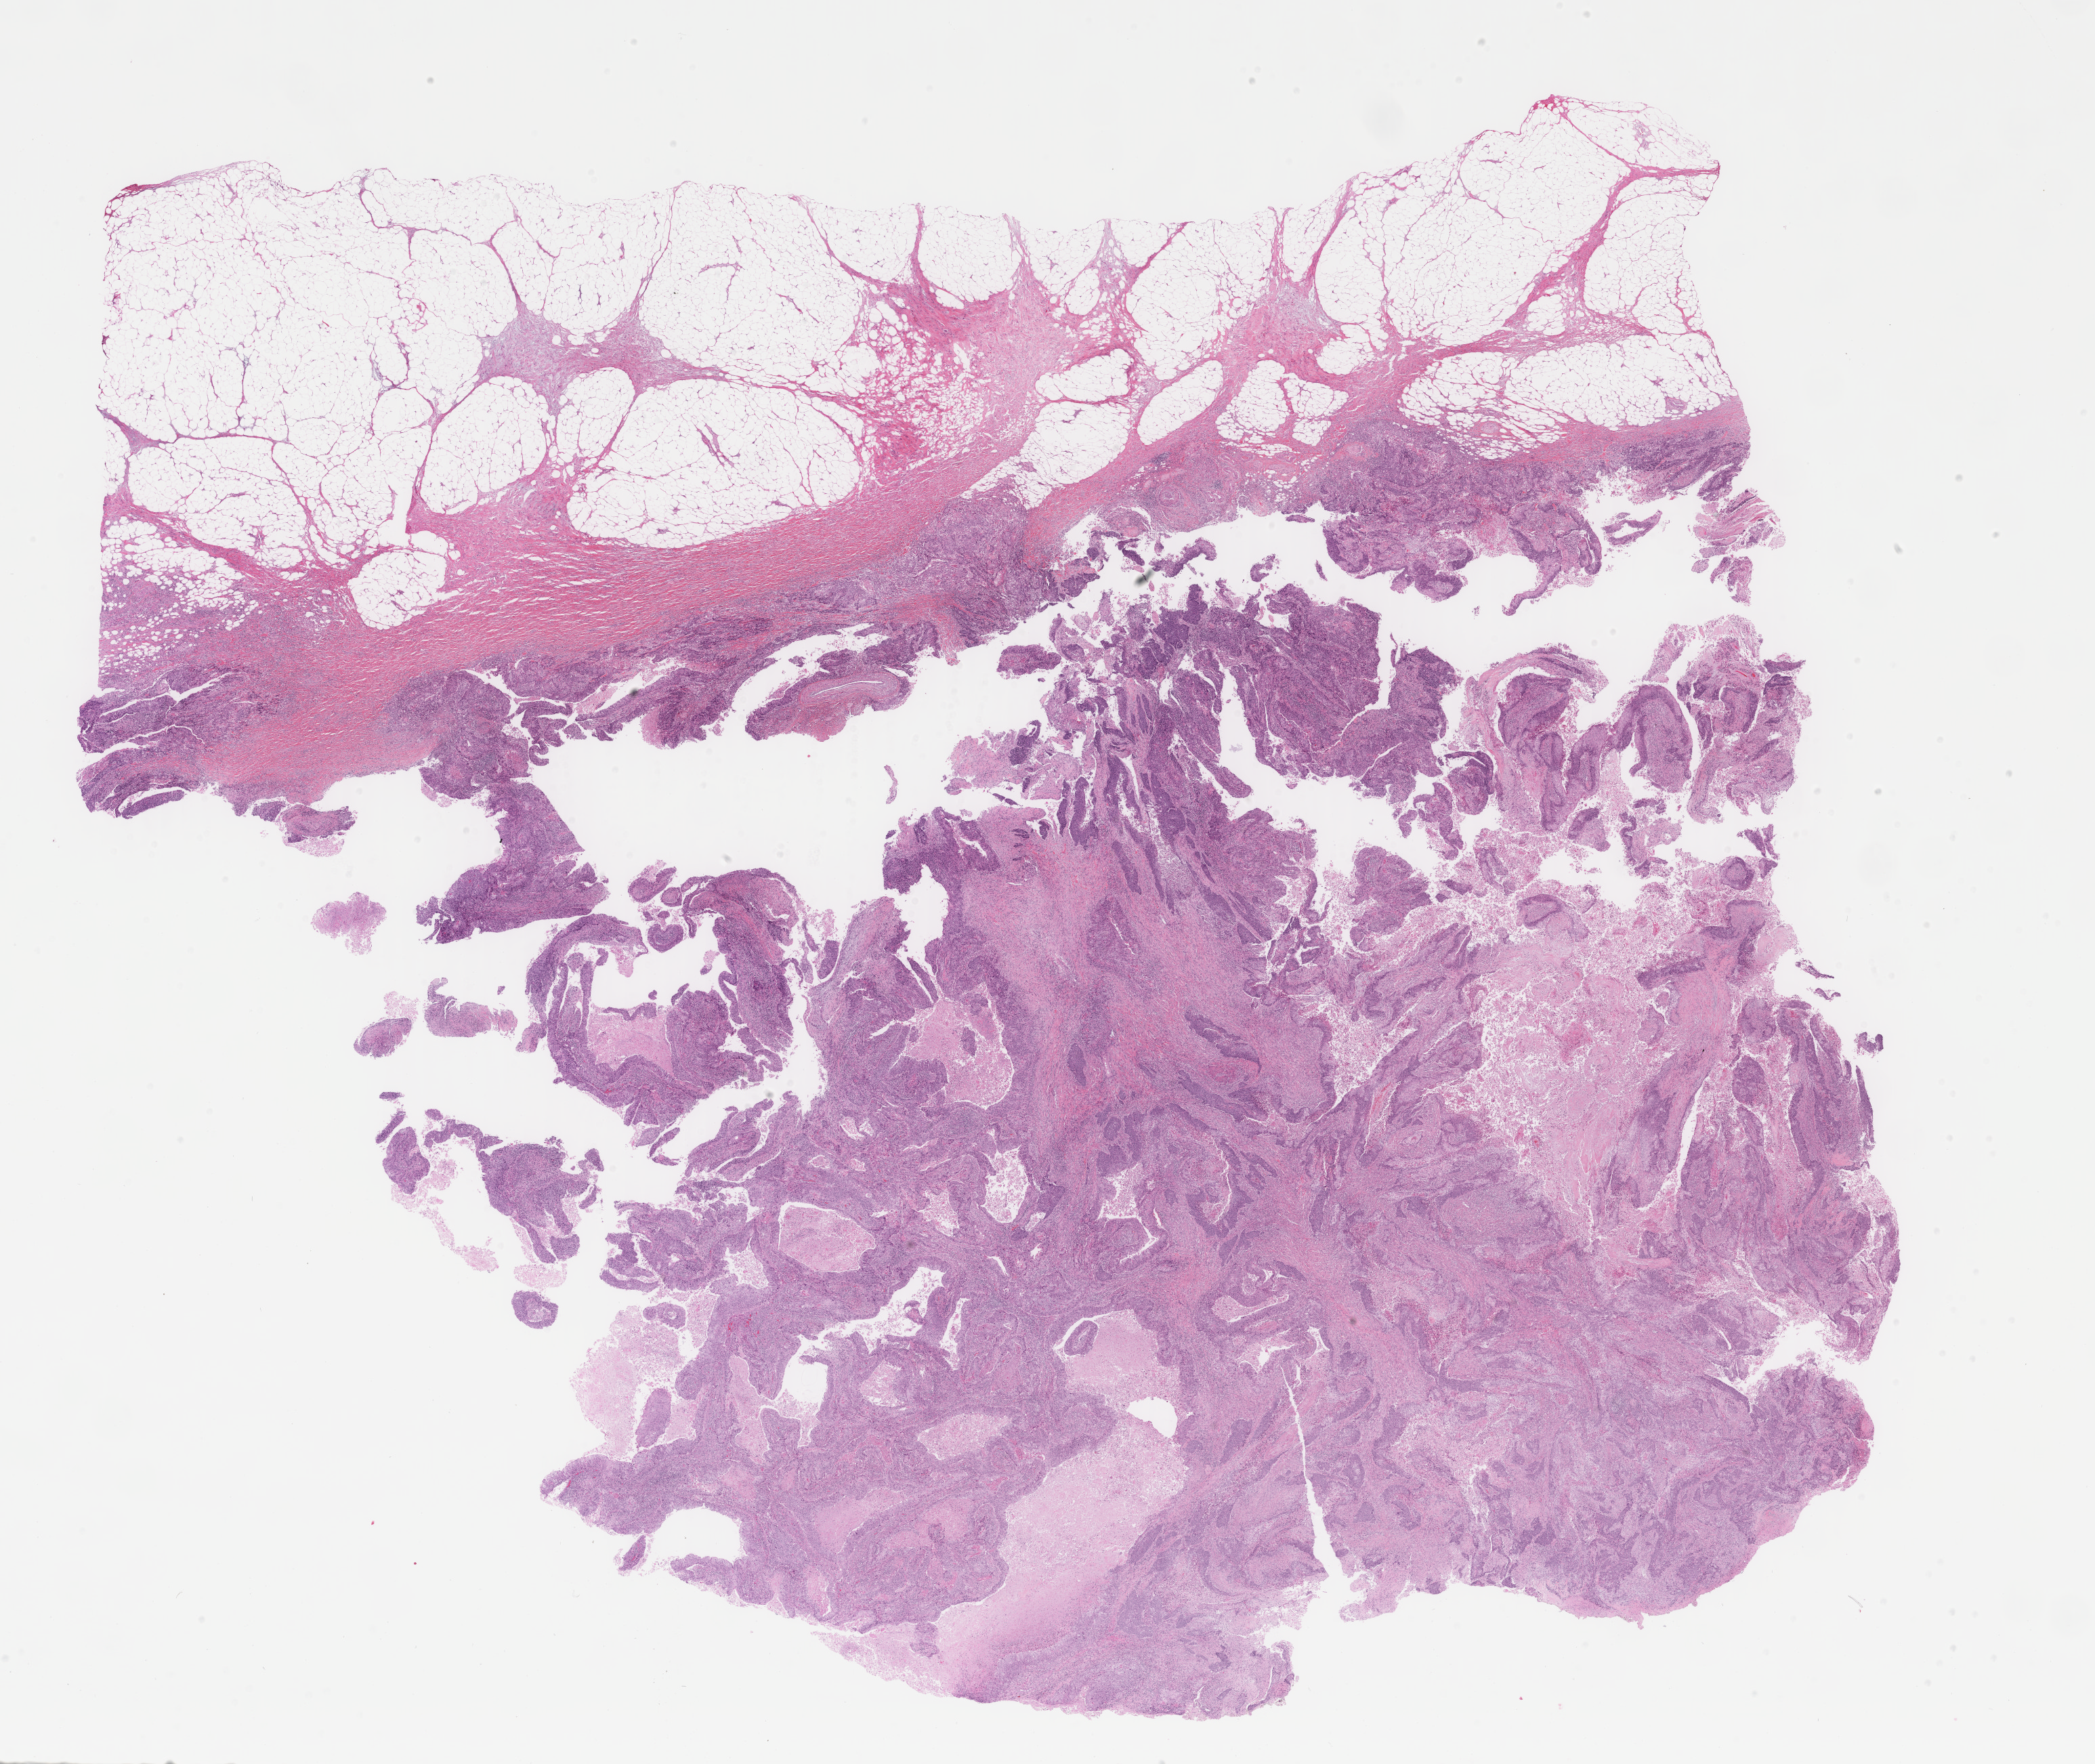
H&E-stained whole-slide image, a low-resolution overview of the entire scanned area, about 24.6 x 20.7 mm. FFPE section. Primary tumour sample from the bladder. Patient: male, age at initial diagnosis 85 years. Histologic grade: high grade.
Diagnosis: Transitional cell carcinoma. TNM: T3b N0 M0. AJCC pathologic stage: II.